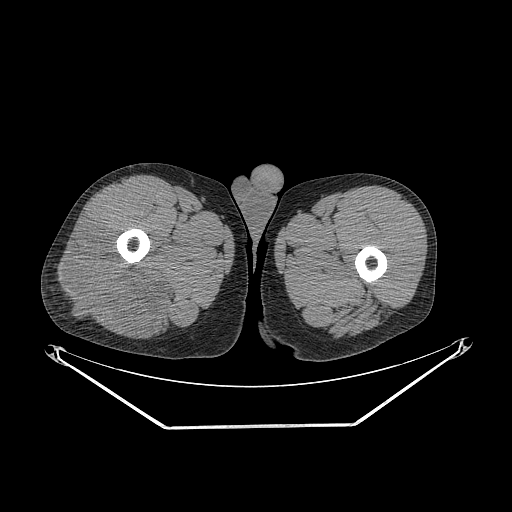
CT of an extremity soft-tissue mass (from a PET/CT study), one axial slice. Reconstruction kernel STANDARD. Soft-tissue window (W 400 / L 40 HU). 3.75 mm slice thickness. 512 × 512 image matrix. Male patient. From the clinical record (not read from this slice): histological type: poorly differentiated synovial sarcoma; grade: high; site of the primary tumour: right buttock.
Annotated regions visible in this slice (expert contour drawn on MRI and transferred to this co-registered scan by the dataset authors):
- gross tumour volume including surrounding oedema: box from (x=55, y=221) to (x=177, y=334) px
- gross tumour volume (mass): (x=55, y=221)–(x=163, y=334)